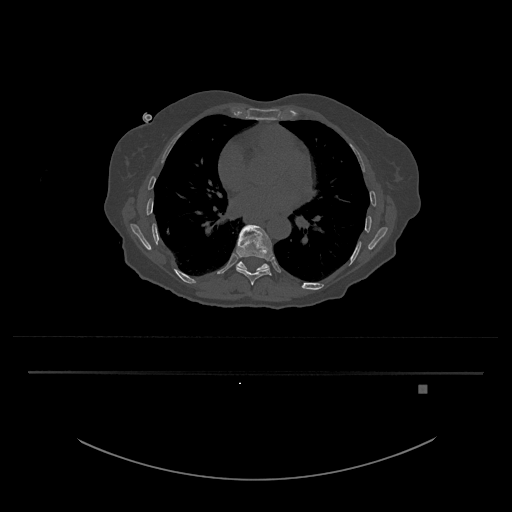
CT including the spine, one axial slice. Position 748 of 797 along the scan axis. Reconstruction kernel Br40s/3. 120 kVp. Bone window (W 1800 / L 400 HU). 0.5 mm slice thickness. 512 × 512 image matrix. Patient: female, 57 years. From the clinical record (not read from this slice): primary cancer: cervical.
Annotated regions visible in this slice (semi-automatically segmented with operator editing):
- T10 vertebra: box from (x=236, y=261) to (x=270, y=272) px
- T9 vertebra: (x=236, y=224)–(x=273, y=286)